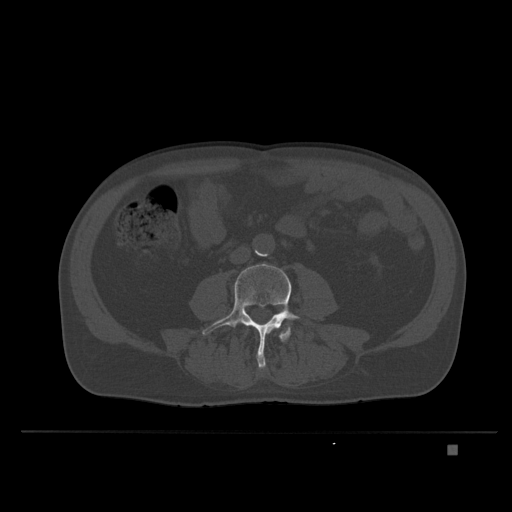
CT including the spine, one axial slice; position 77 of 435 along the scan axis; bone window (W 1800 / L 400 HU); 512 × 512 image matrix, field of view 434 × 434 mm. Male patient, age 73 years. From the clinical record (not read from this slice): primary cancer: skin.
Structures marked on this image (semi-automatically segmented with operator editing):
- L3 vertebra: bounding box <246,327,278,332> (left, top, right, bottom; pixels)
- L4 vertebra: <202,263,300,370>